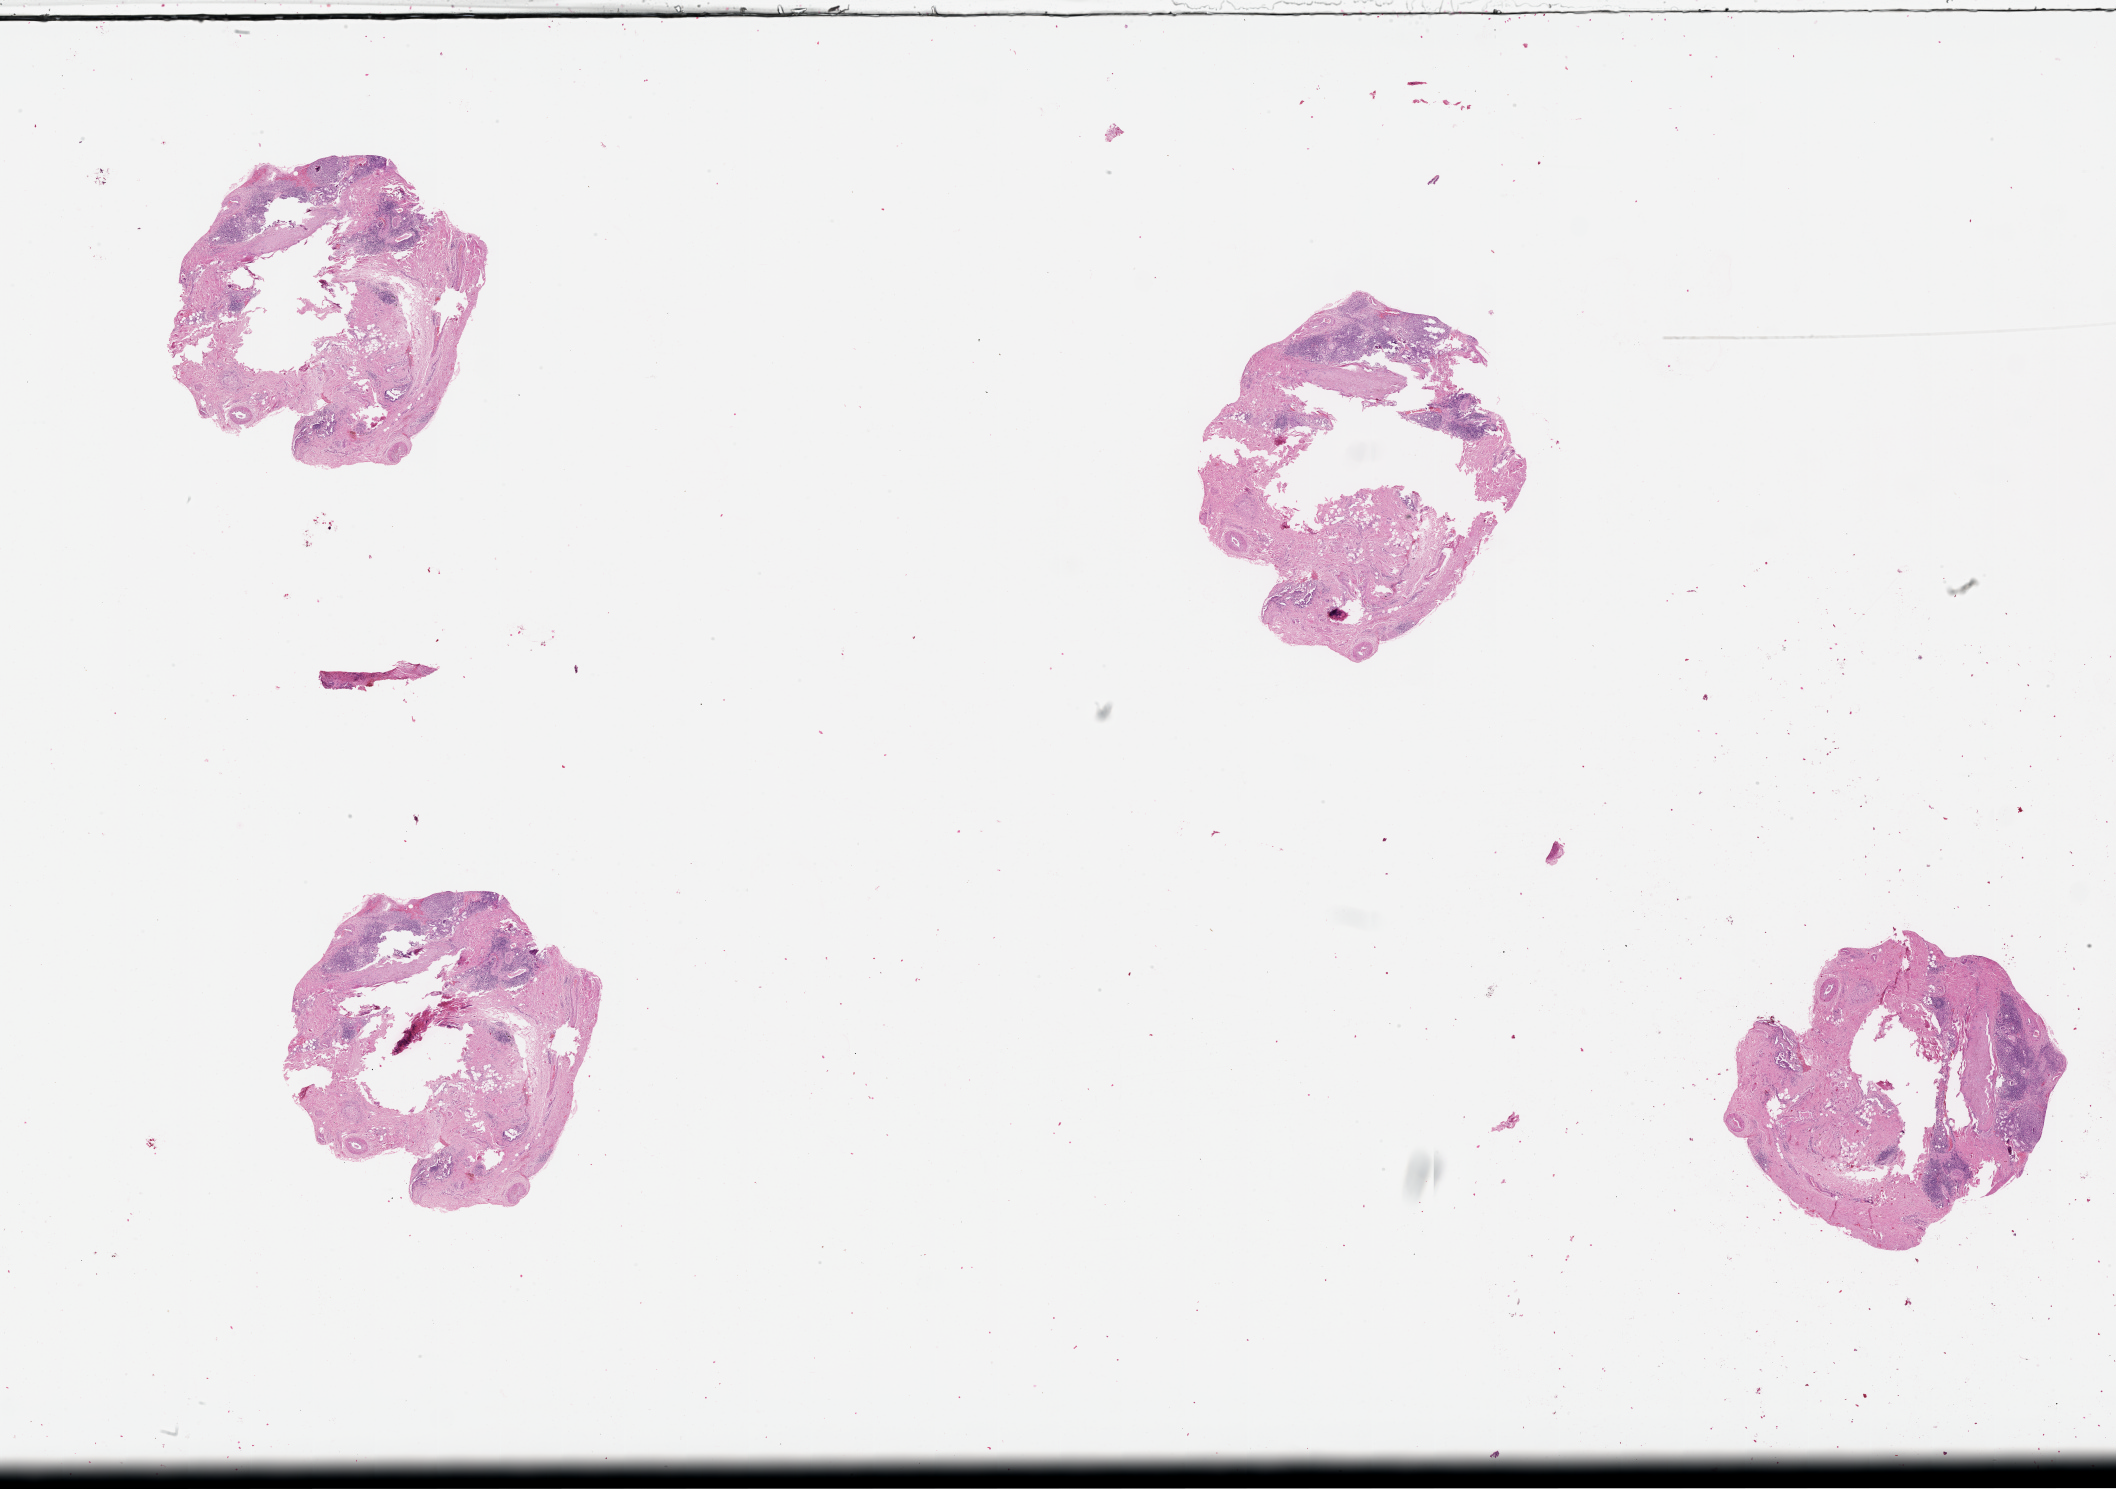
H&E-stained whole-slide image, low-resolution overview of the scanned area, about 34.1 x 24.0 mm (from a 20x scan); lung, tumour tissue. 59-year-old male patient.
Patient diagnosis (cohort enrolment): squamous cell carcinoma (lung).